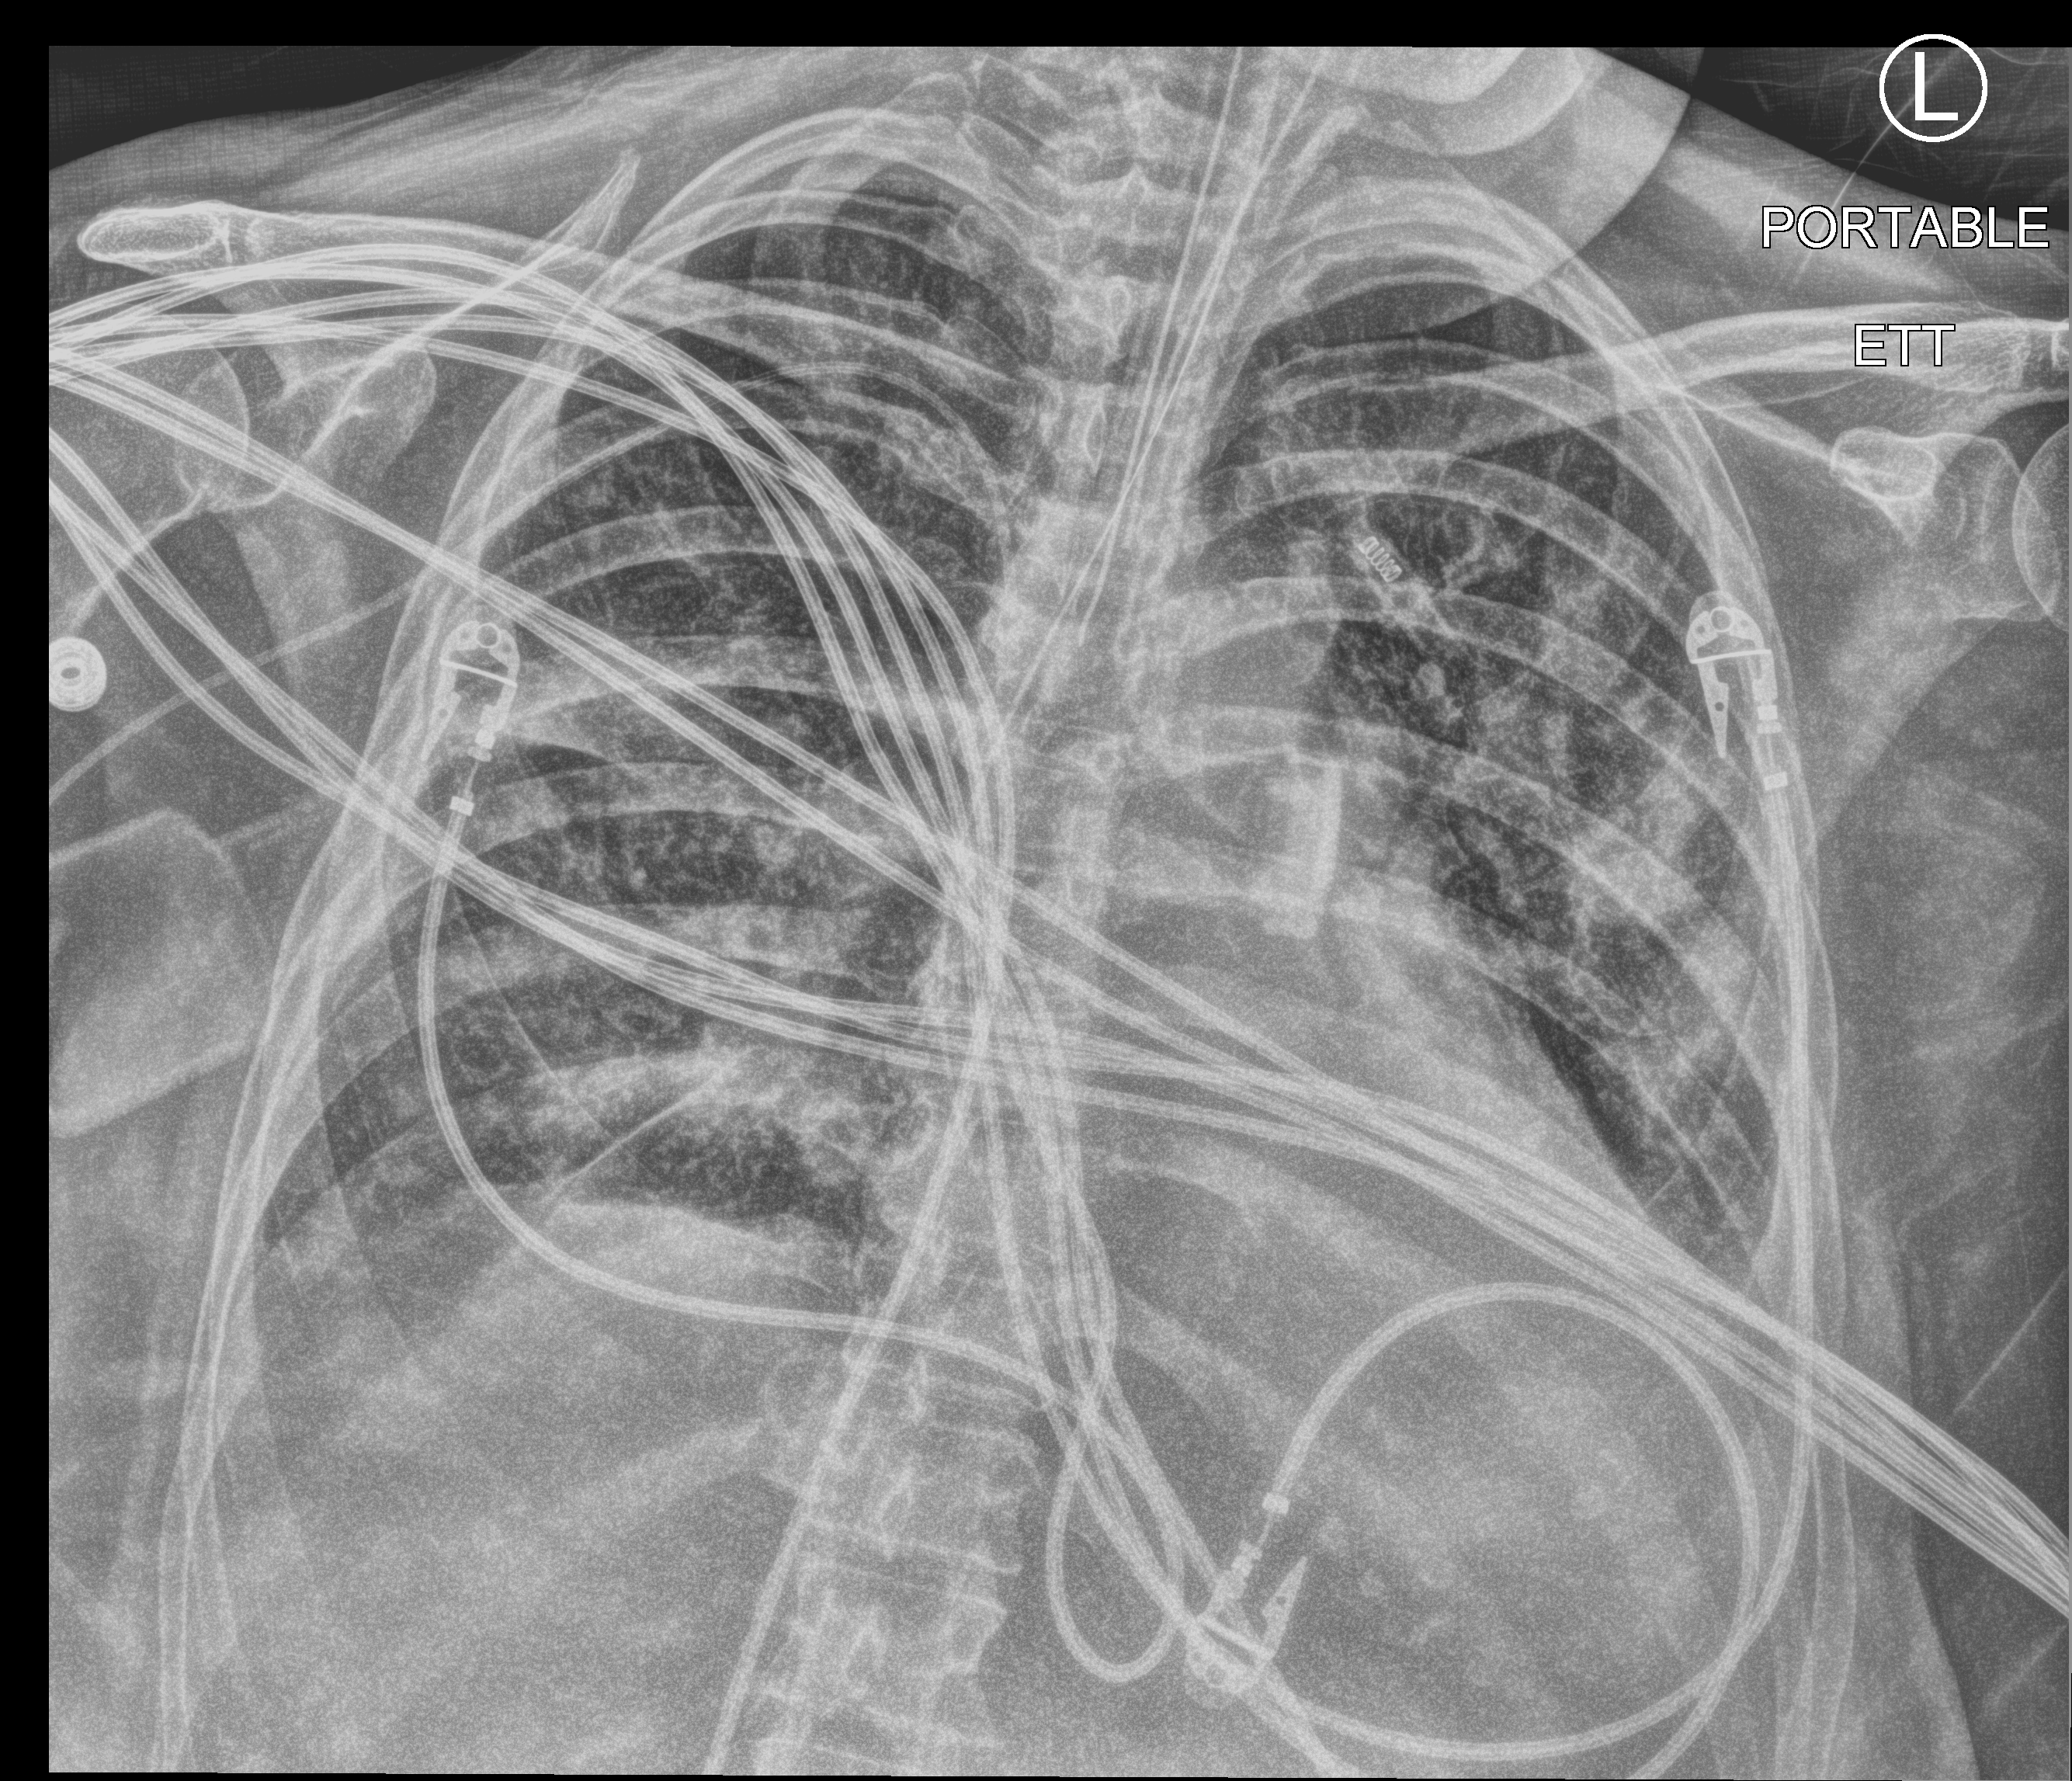
Portable chest radiograph, anteroposterior (AP) projection. Female patient hospitalised with COVID-19, age 60–74 years.
From the hospital-stay record, not from the radiograph (when in the stay this image was taken is not recorded):
- mechanically ventilated during this hospital stay: yes